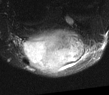
MRI of an extremity soft-tissue mass, one axial slice; position 18 of 52 along the scan axis; T2-weighted fat-saturated; MR volume resampled by the dataset authors to the PET/CT grid (not the native acquisition matrix); 3.27 mm slice thickness; 109 × 95 image matrix. Male patient. Case-level facts recorded for this patient, not image findings: histological type: synovial sarcoma; site of the primary tumour: left poplietal fossa.
Outlined on this slice (expert contour drawn on MRI and transferred to this co-registered scan by the dataset authors):
- gross tumour volume (mass): bounding box [x1, y1, x2, y2] px = [19, 29, 86, 71]